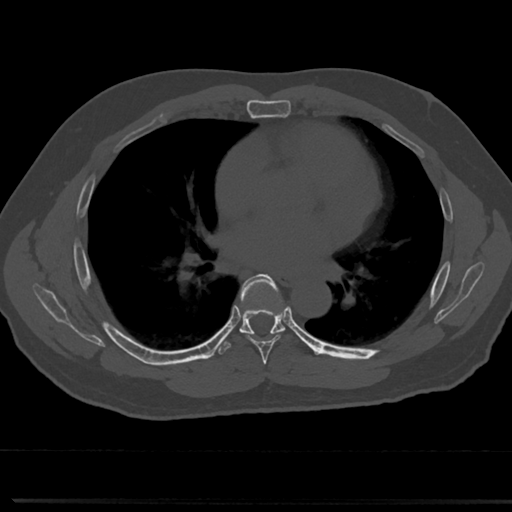
CT including the spine, one axial slice; 120 kVp; bone window (W 1800 / L 400 HU); 512 × 512 image matrix, field of view 355 × 355 mm. Patient: male, 61 years. From the clinical record (not read from this slice): primary cancer: prostate.
Outlined on this slice (semi-automatically segmented with operator editing):
- T5 vertebra: bounding box [x1, y1, x2, y2] px = [265, 370, 271, 376]
- T6 vertebra: [238, 276, 289, 357]
- T7 vertebra: [241, 326, 284, 334]